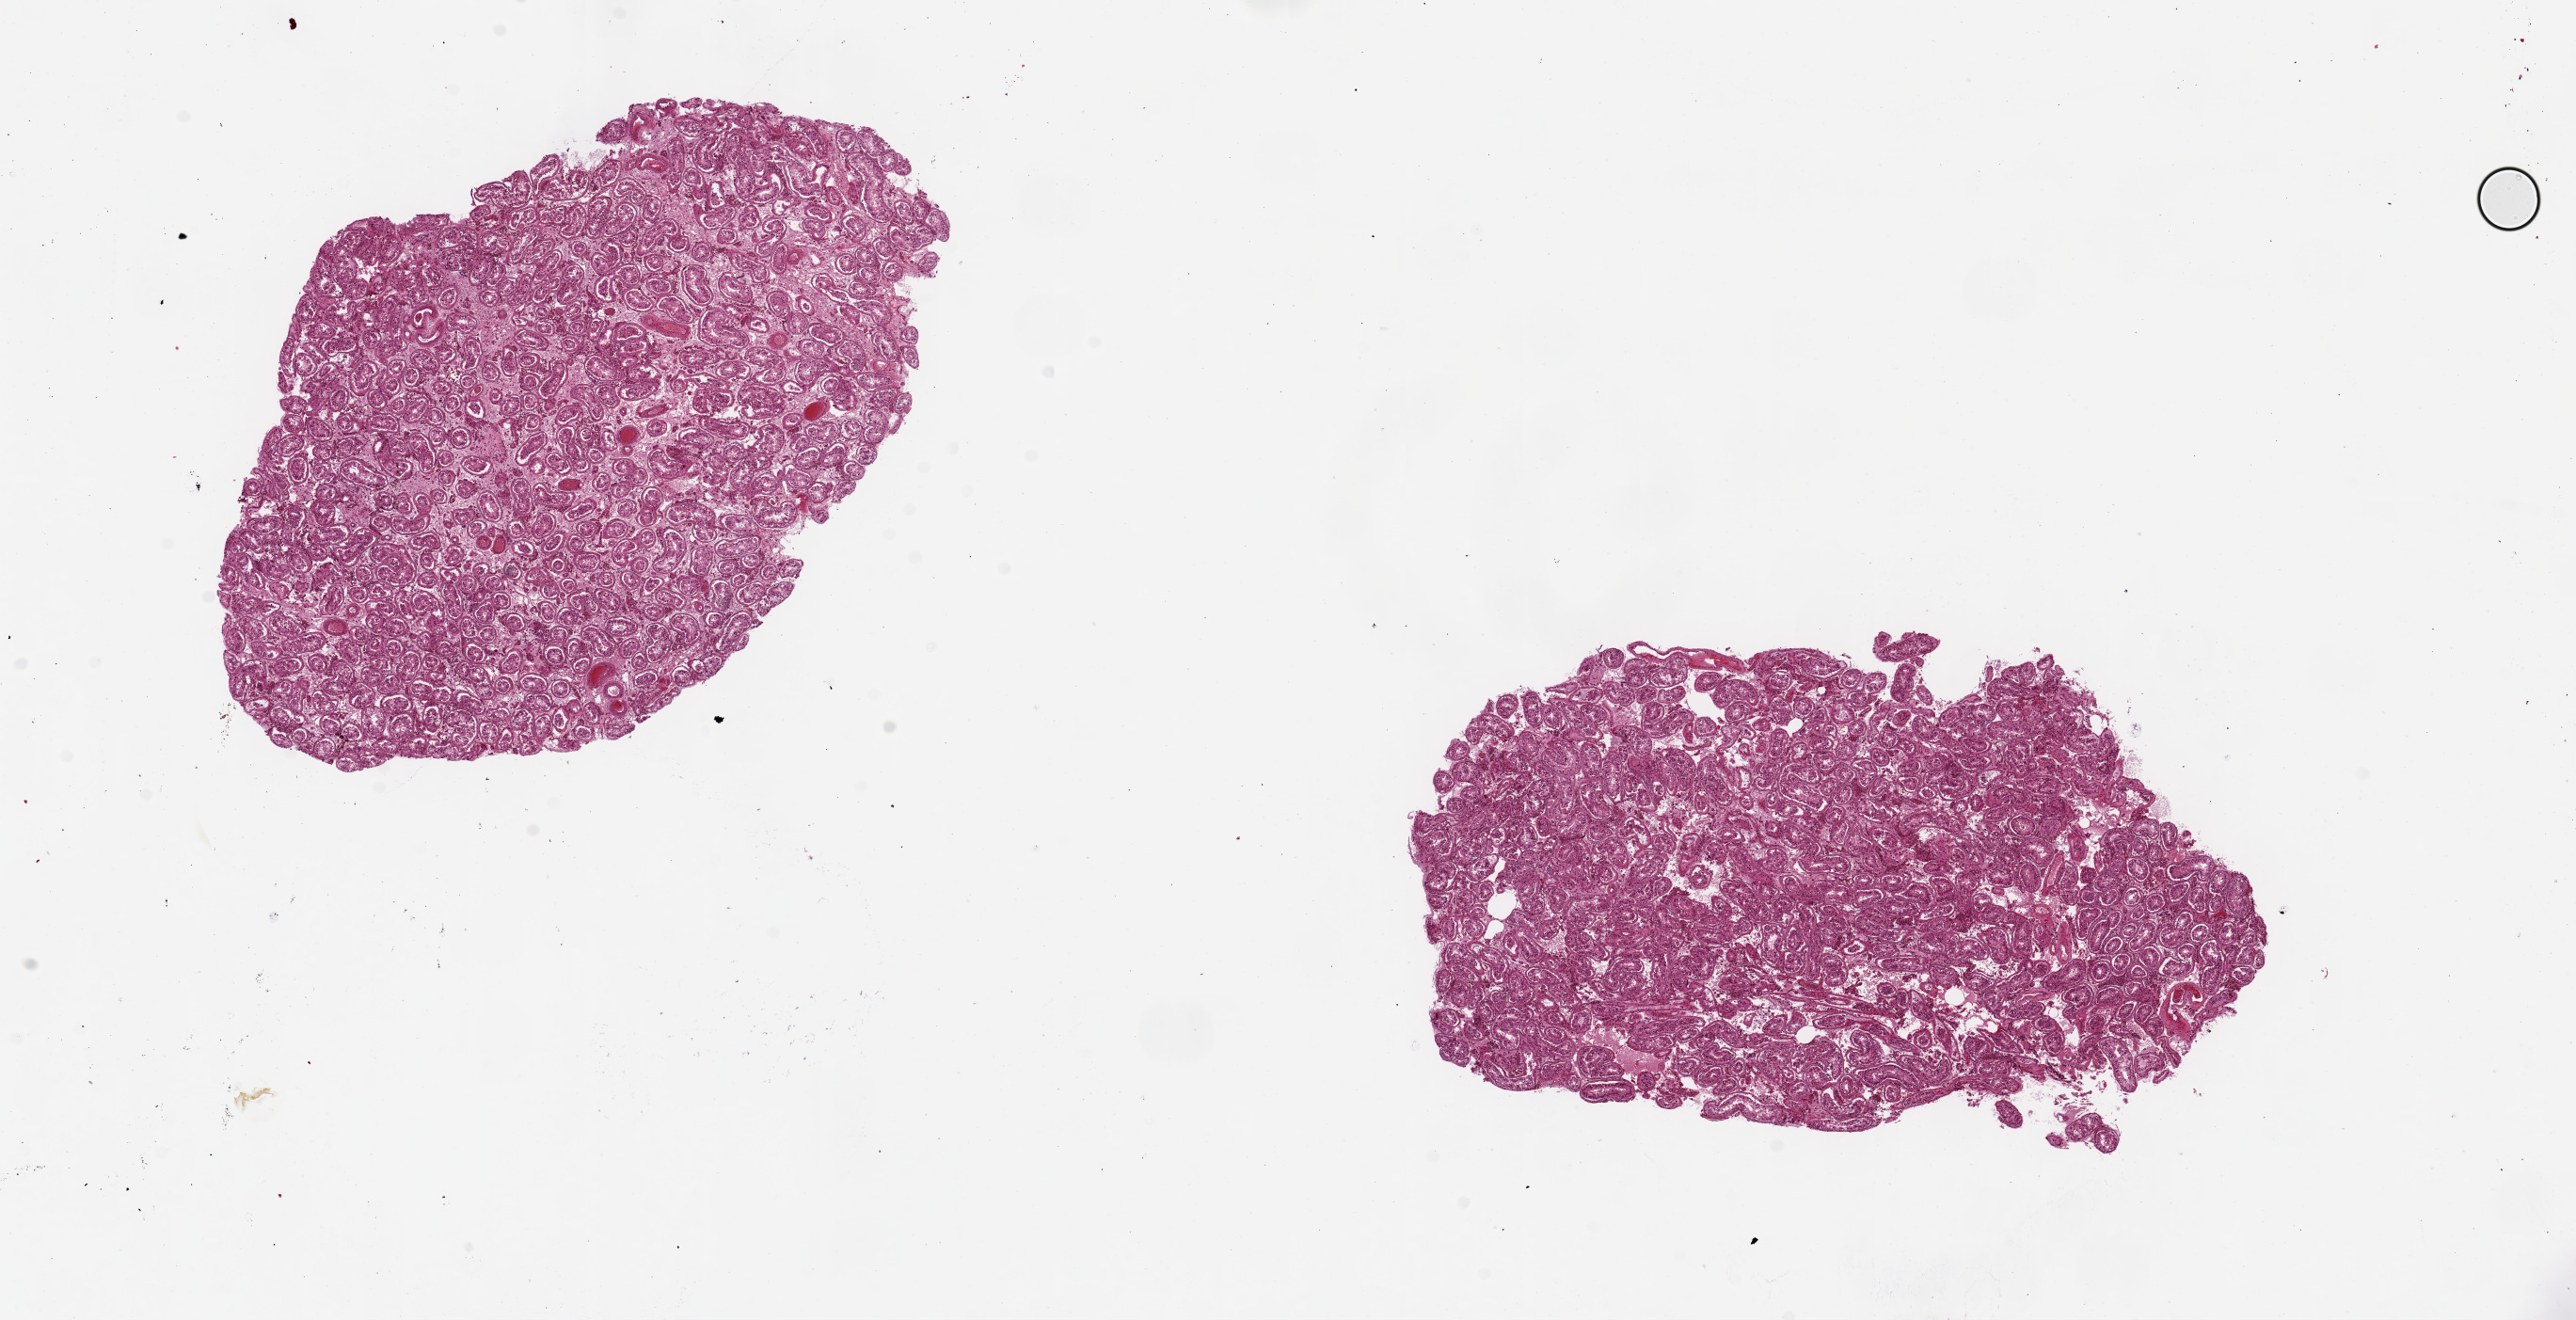
Hematoxylin and eosin (H&E) whole-slide image, low-resolution overview of the scanned area, about 21.7 x 11.1 mm (slide scanned at 20x). PAXgene-fixed, paraffin-embedded tissue. Target tissue: testis. Donor tissue sample. Male donor.
- pathologist's review note for this sample: 2 pieces, 7x5 & 7x5mm; reduced spermatogenesis